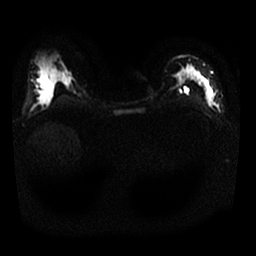
Breast MRI, one axial slice; position 16 of 25 along the scan axis; diffusion-weighted series; image 2 of 4 stored at this slice position (different b-values; order by instance number); 1.5 T; 4 mm slice thickness; 256 × 256 image matrix, field of view 320 × 320 mm. Female patient.
Structures marked on this image (manually delineated by an expert):
- tumour on diffusion-weighted imaging: box from (x=202, y=78) to (x=213, y=98) px